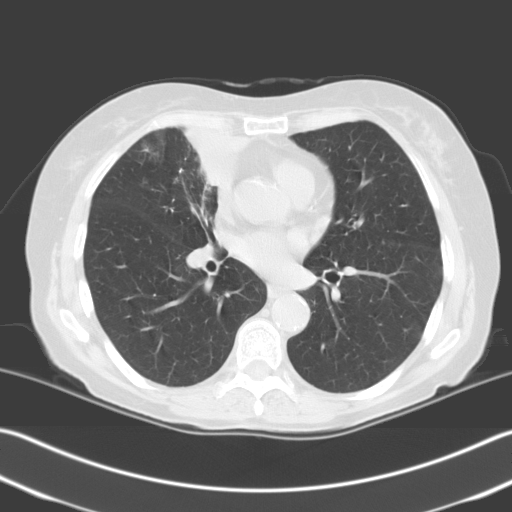
Low-dose screening chest CT, one axial slice; position 112 of 204 along the scan axis; 140 kVp; lung window (W 1500 / L -600 HU); 3.2 mm slice thickness; 512 × 512 image matrix.
Annotated regions visible in this slice (expert manual segmentation):
- lesion 1 (tumor, upper lobe of right lung): bounding box <185,131,247,185> (left, top, right, bottom; pixels)